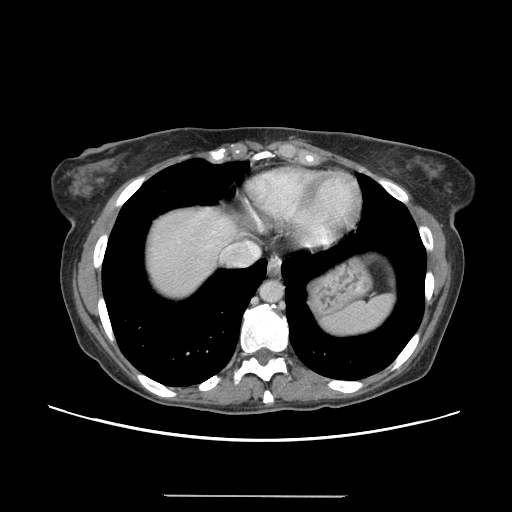
Contrast-enhanced abdominal CT, one axial slice; slice 131 of 144 in the series (ordered by position); intravenous contrast given; soft-tissue window (W 400 / L 40 HU); 2.5 mm slice thickness; 512 × 512 image matrix, field of view 380 × 380 mm. Female patient, age 53 years. From the clinical record (not read from this slice): diagnosis: colorectal cancer liver metastases, imaged before liver resection; multiple liver metastases: yes.
Annotated regions visible in this slice (manually delineated by an expert):
- hepatic veins: bounding box [x1, y1, x2, y2] px = [229, 242, 259, 257]
- liver: [143, 207, 237, 300]
- planned liver remnant (the part of the liver to remain after resection): [144, 205, 240, 287]